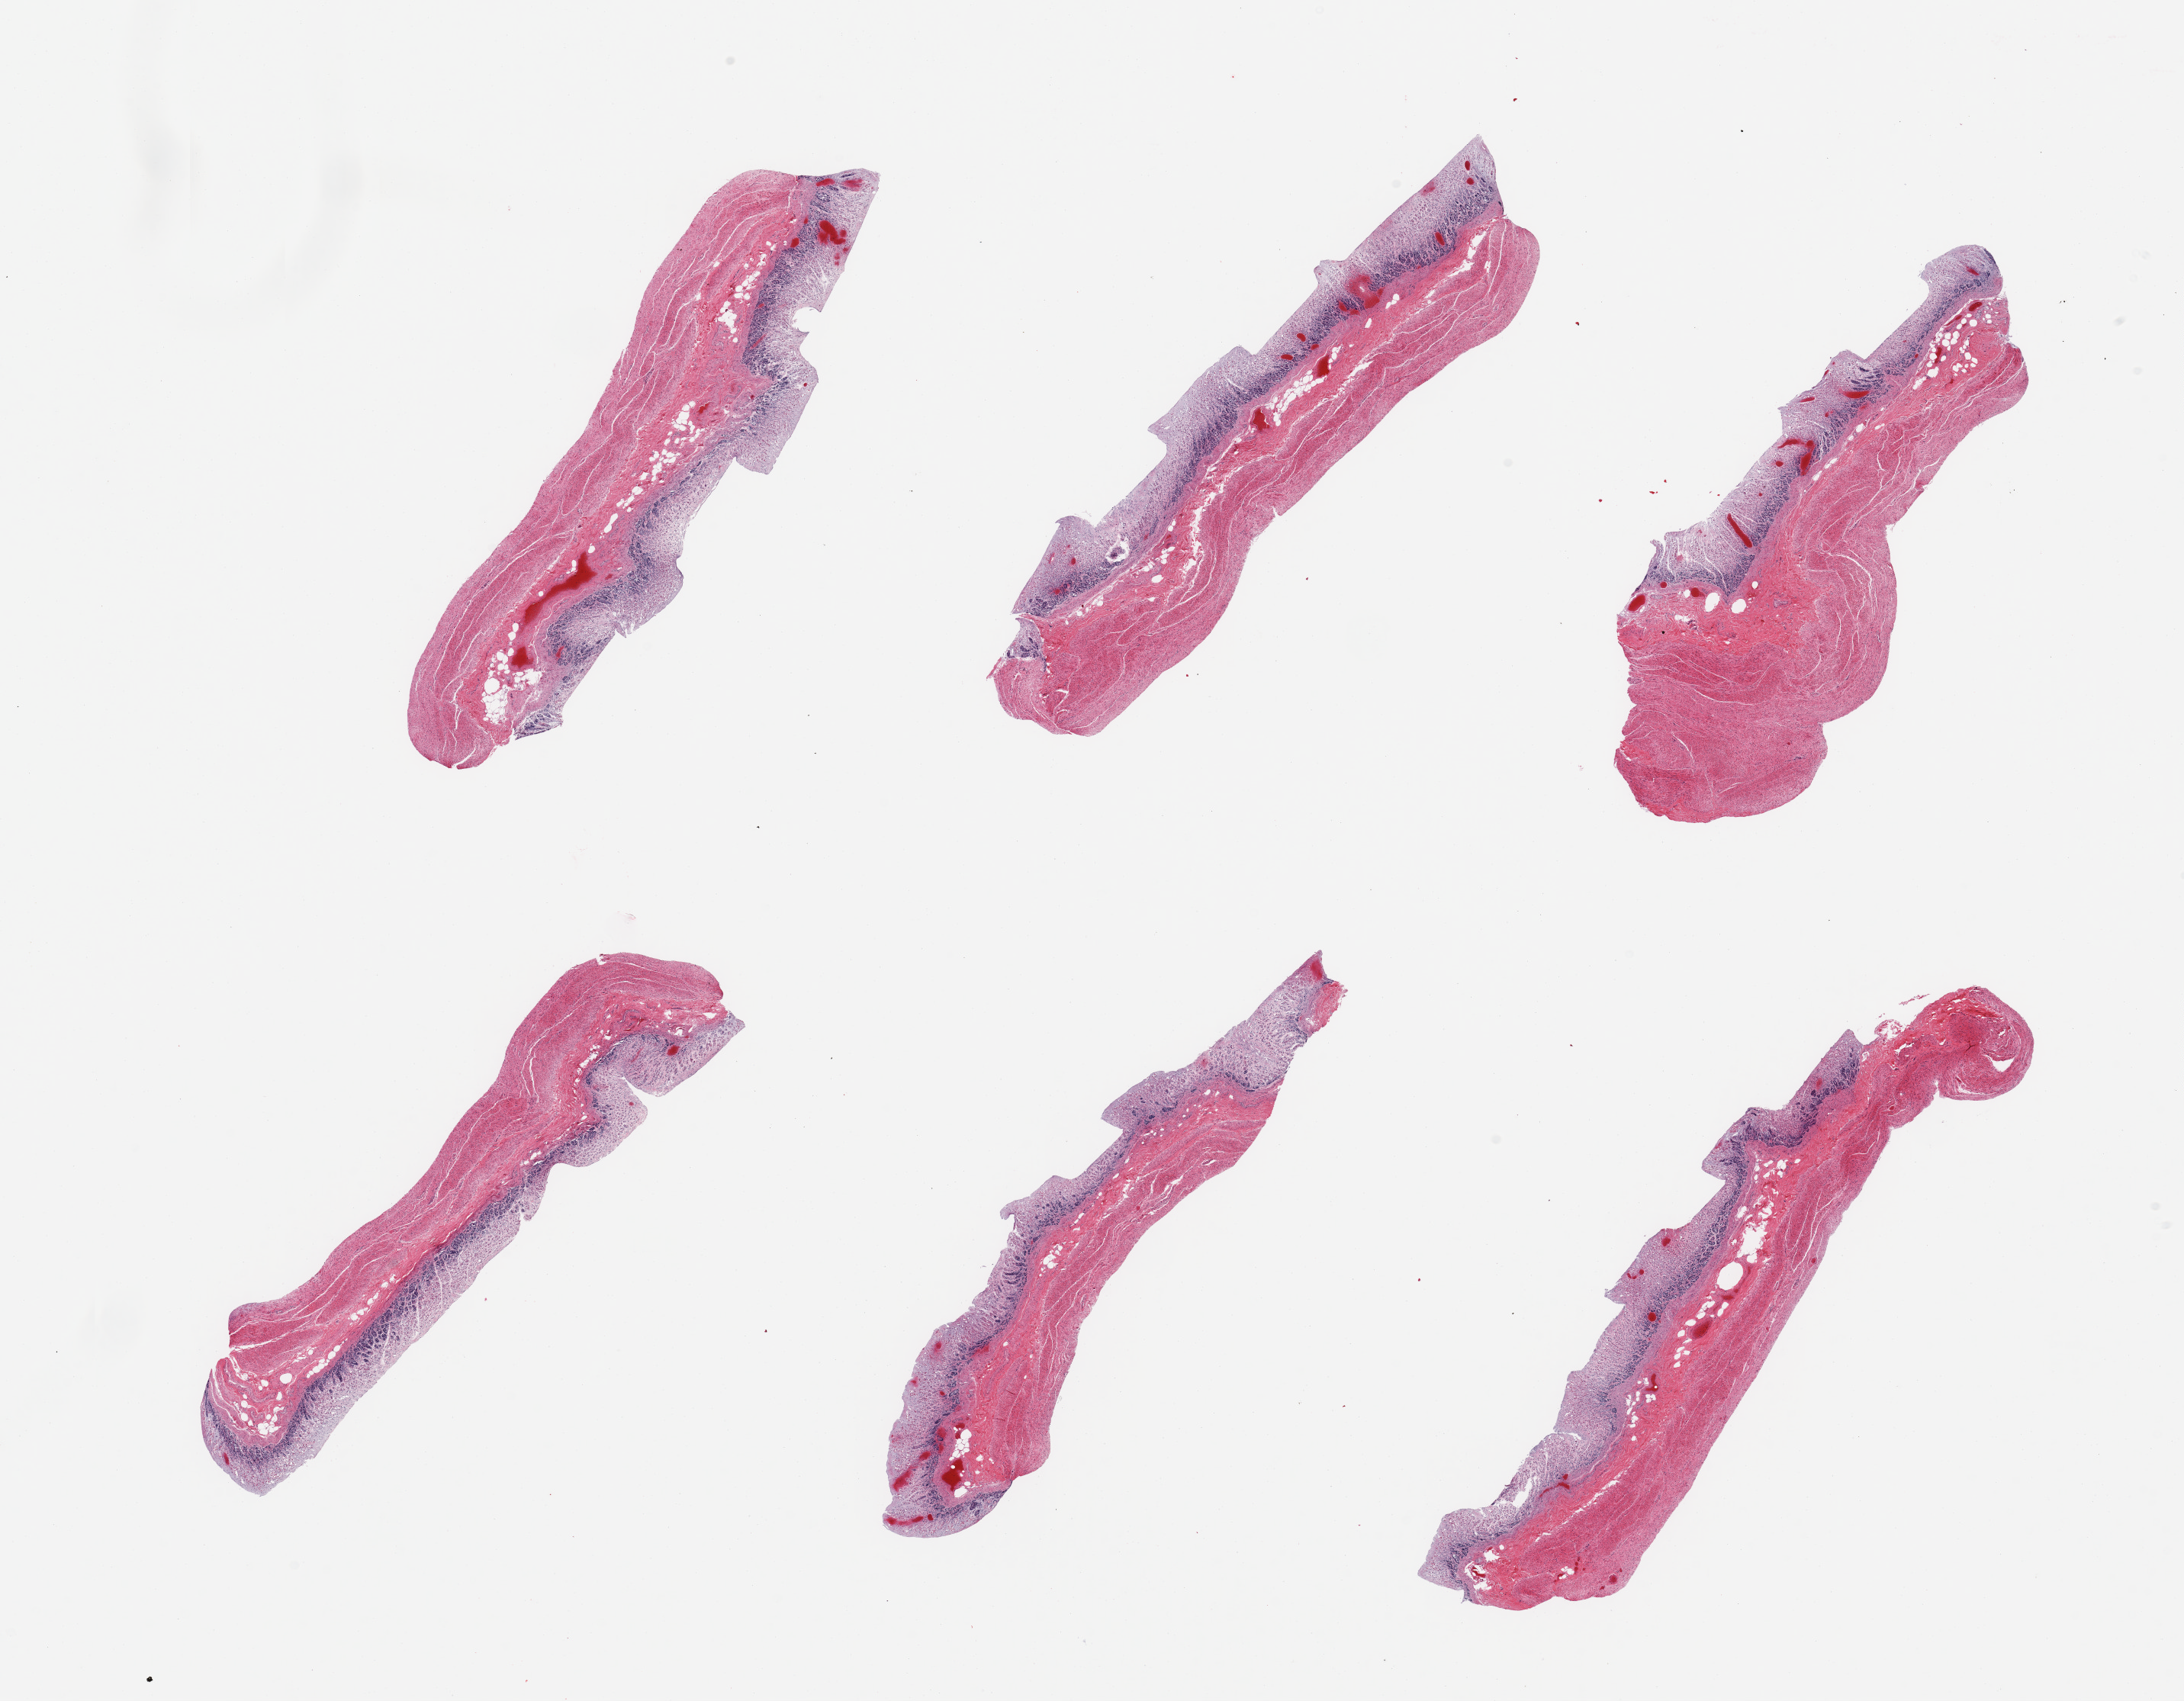
H&E whole-slide image, brightfield, whole scanned area (about 22.6 x 17.6 mm, from a 20x scan) shown as a low-resolution overview; PAXgene-fixed paraffin-embedded (PFPE) section; section of stomach (target tissue); tissue donor sample. Donor sex: female.
* reviewer comment on this tissue sample: 6 pieces; mucosa=3;muscle=2